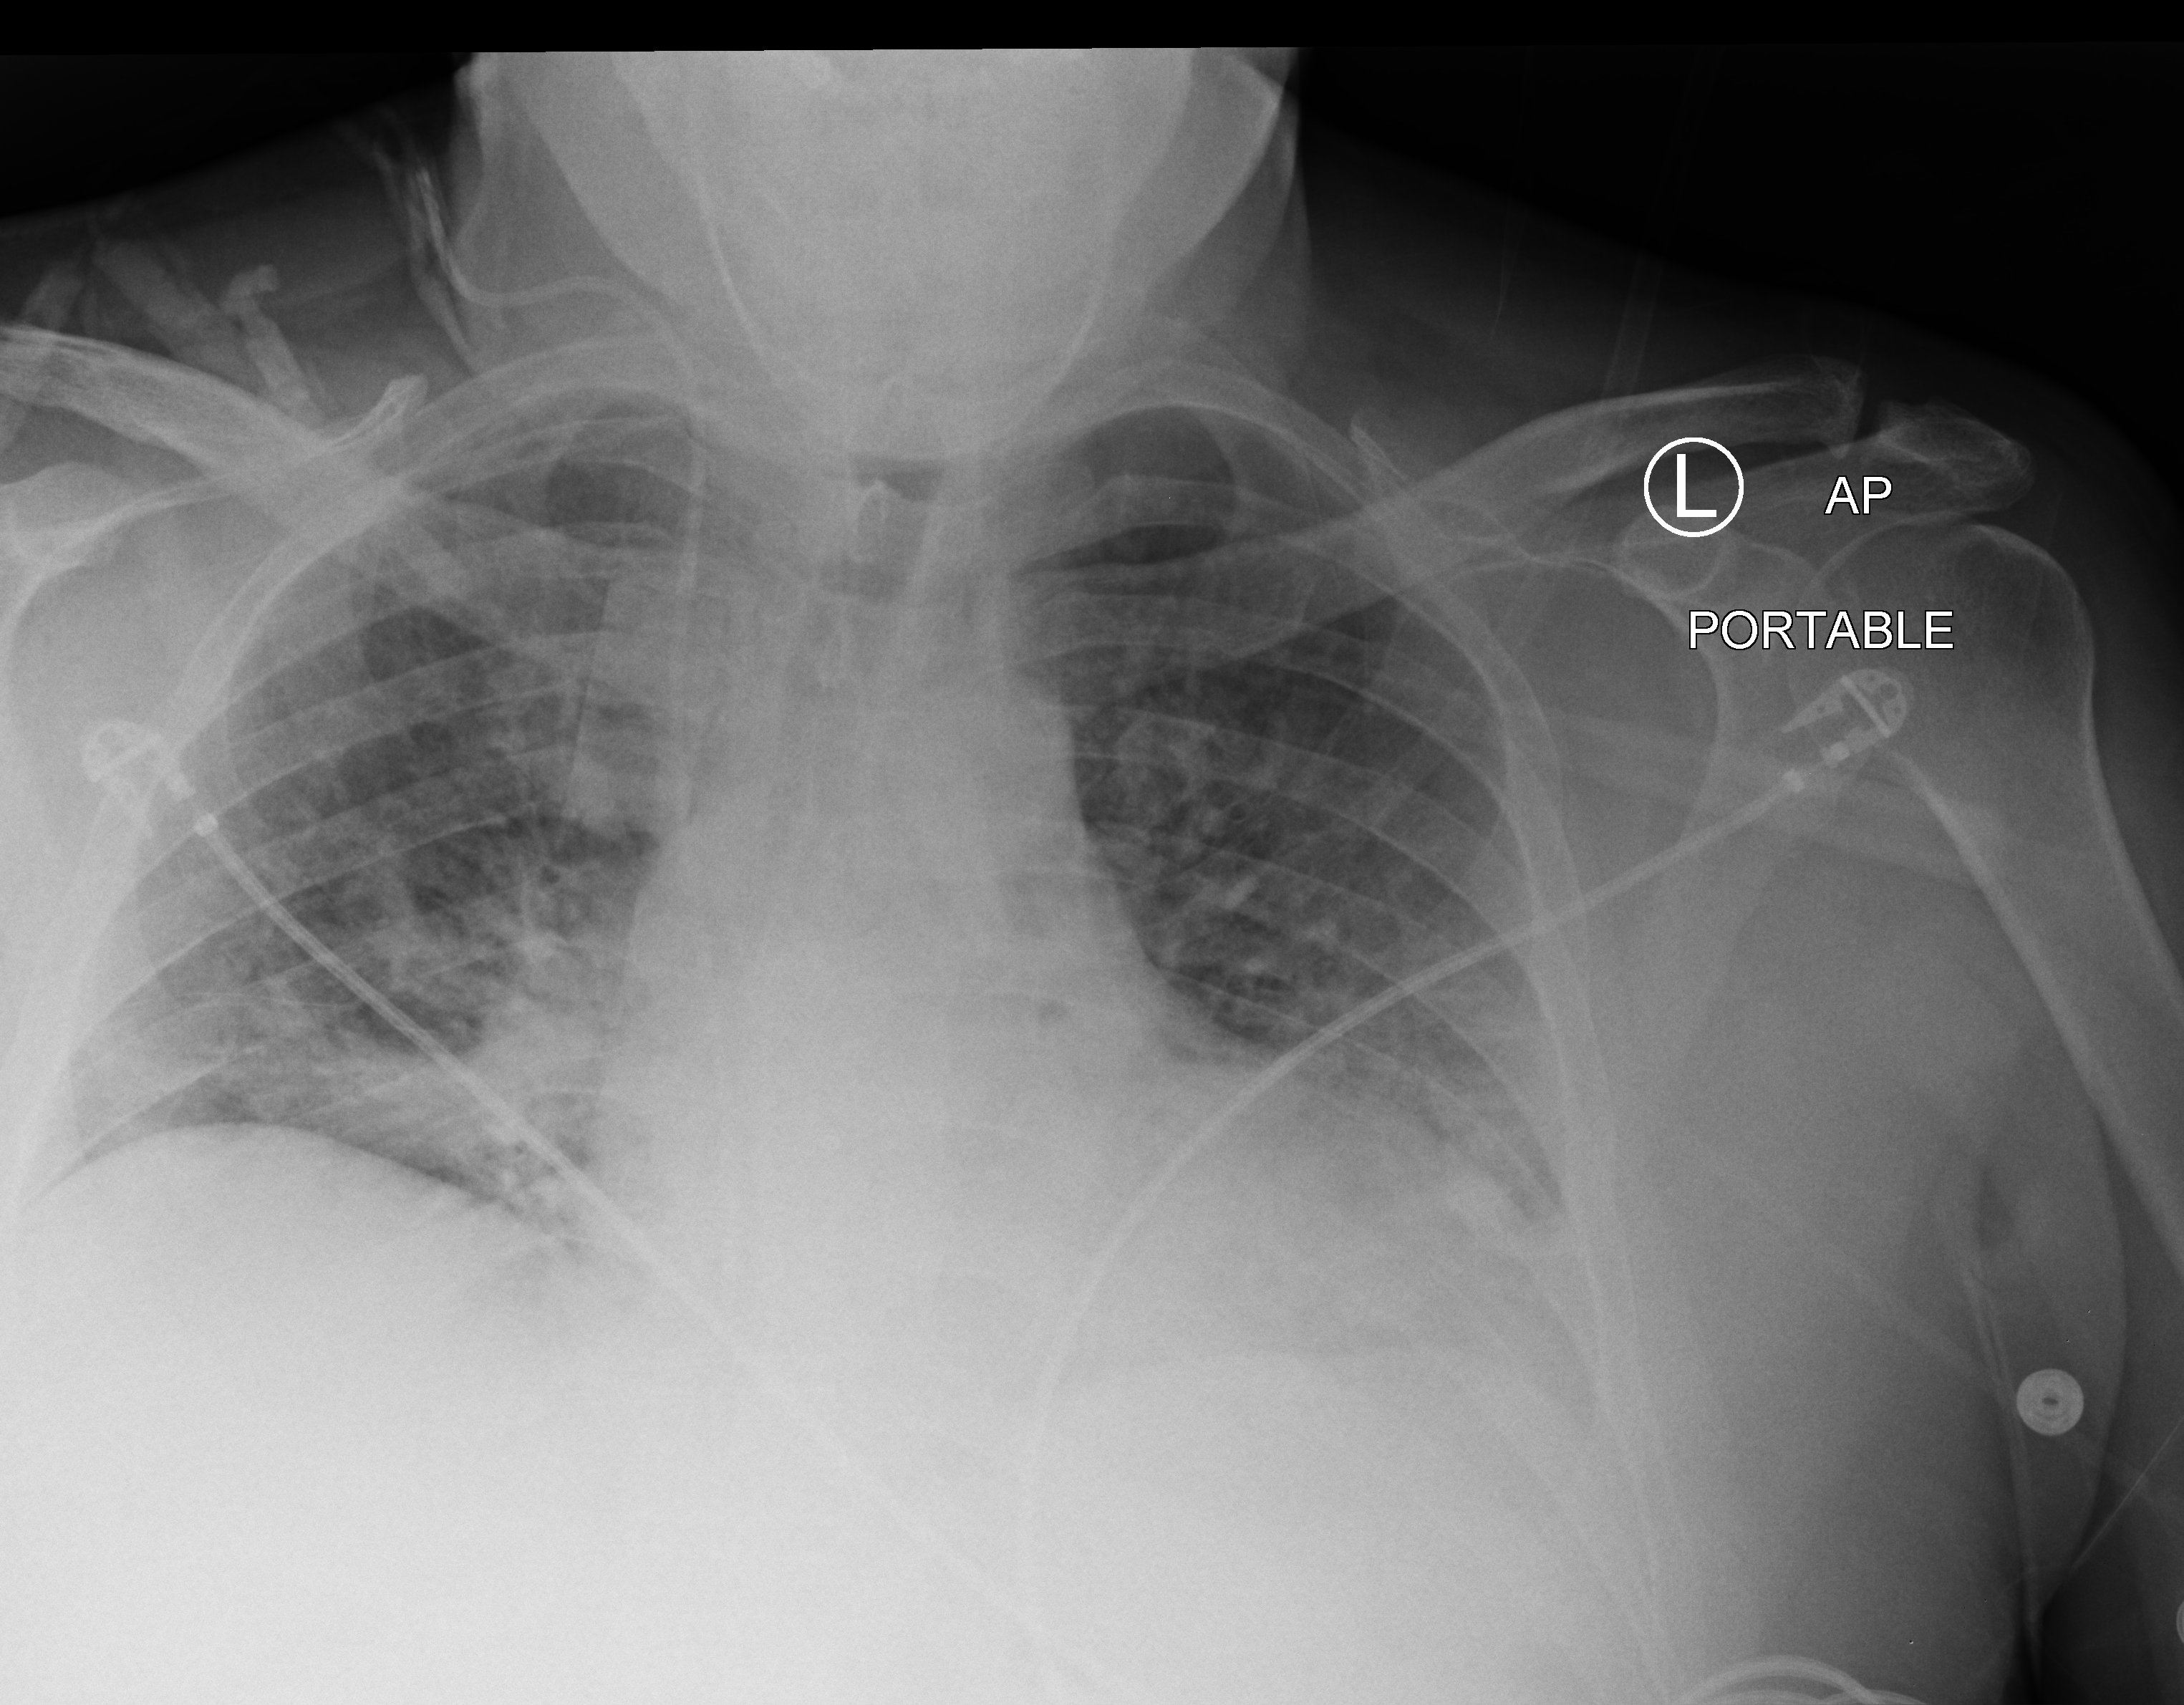
Chest X-ray (portable), anteroposterior (AP) projection. Male patient hospitalised with COVID-19, age 18–59 years.
Hospital-stay facts (about this admission, not read from this image; timing relative to this image not recorded):
- smoking status (admission record): never
- mechanically ventilated during this hospital stay: yes
- admitted to intensive care during this hospital stay: yes